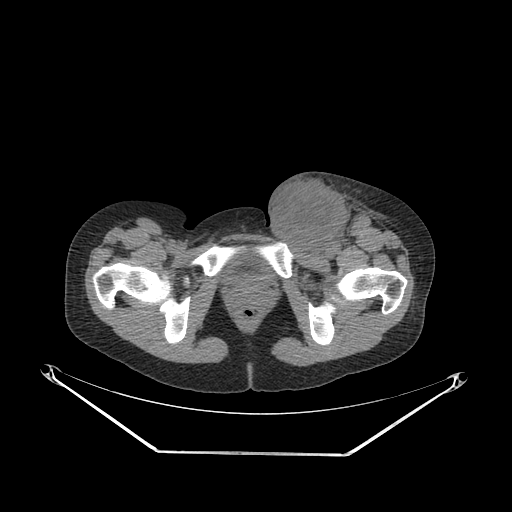
CT of an extremity soft-tissue mass (from a PET/CT study), one axial slice. Reconstruction kernel SOFT. 140 kVp. Soft-tissue window (W 400 / L 40 HU). 3.75 mm slice thickness. 512 × 512 image matrix. Female patient. Case-level facts recorded for this patient, not image findings: histological type: leiomyosarcoma; grade: high; site of the primary tumour: groin.
Structures marked on this image (expert contour drawn on MRI and transferred to this co-registered scan by the dataset authors):
- gross tumour volume including surrounding oedema: bounding box <262,174,384,254> (left, top, right, bottom; pixels)
- gross tumour volume (mass): <263,180,348,254>